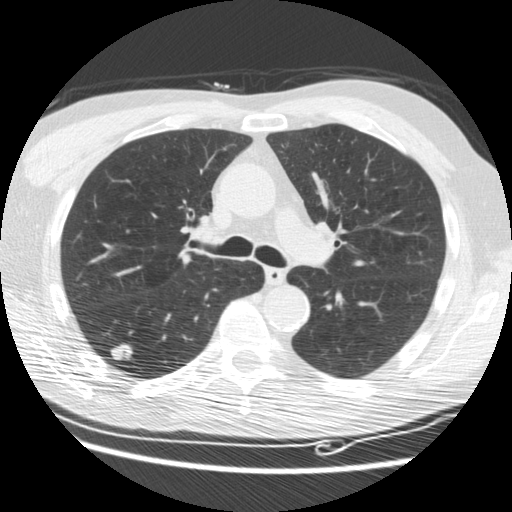
Low-dose screening chest CT, axial slice, third screening round (two years after baseline), lung window (W 1500 / L -600 HU), slice 66 of 176 in the series, 512 × 512 image matrix. Male participant, aged 62 years at enrolment.
Lesion marked by an expert reader, box from (x=102, y=334) to (x=142, y=369) px. The screening reader recorded 3 non-calcified nodules or masses ≥4 mm on this exam (right lower lobe, right lower lobe, right lower lobe); which of them this box marks is not recorded. Later outcome: lung cancer diagnosed 33 days after this screen — adenocarcinoma, NOS, right lower lobe, moderately differentiated (G2), stage IIIB (AJCC 6th edition), 15 mm at pathology.